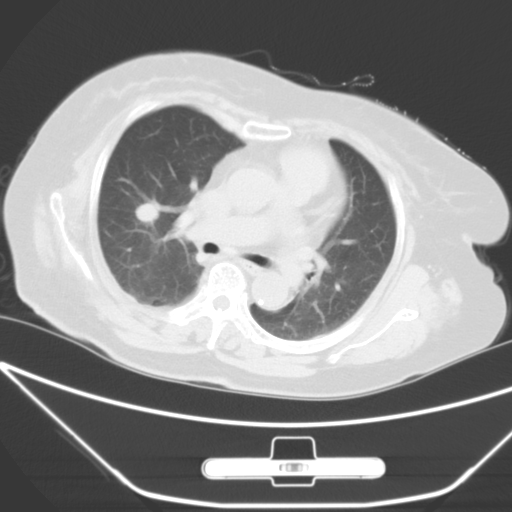
Chest CT, one axial slice. Position 32 of 49 along the scan axis. Lung window (W 1500 / L -600 HU). 5 mm slice thickness. 512 × 512 image matrix, field of view 365 × 365 mm. Patient: female, 65 years. From the clinical record (not read from this slice): clinical TNM (as recorded): T1c N0 M0.
Outlined on this slice (rectangle marked by the reading radiologist):
- lung tumour (recorded histology: adenocarcinoma): box from (x=122, y=185) to (x=166, y=234) px